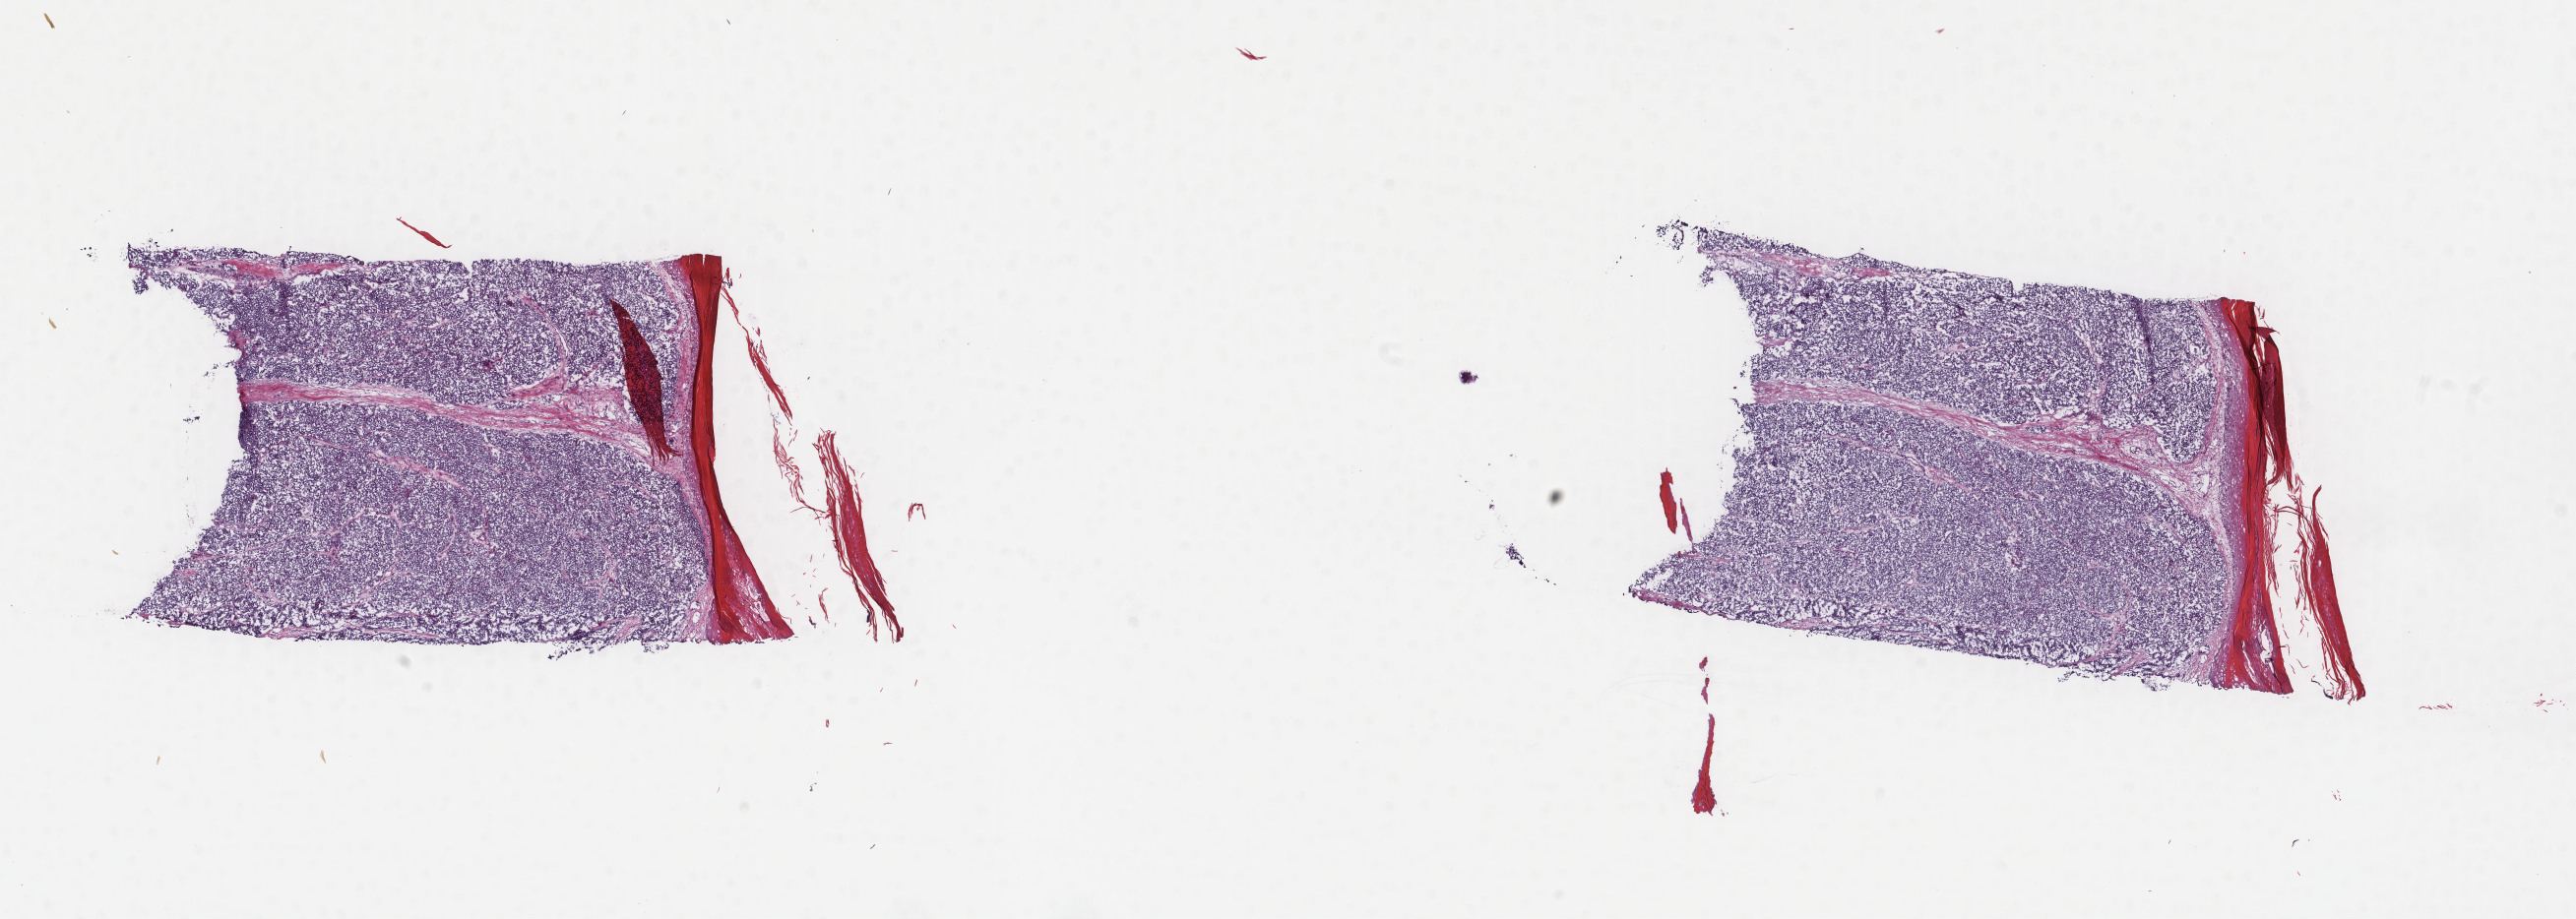
H&E whole-slide image, low-resolution overview of the scanned area, about 20.8 x 7.4 mm (slide scanned at 40x); frozen section from the top of the tissue portion; skin, primary tumour sample. Male patient; age at initial diagnosis 51 years.
Histologic diagnosis: Acral lentiginous melanoma, malignant.